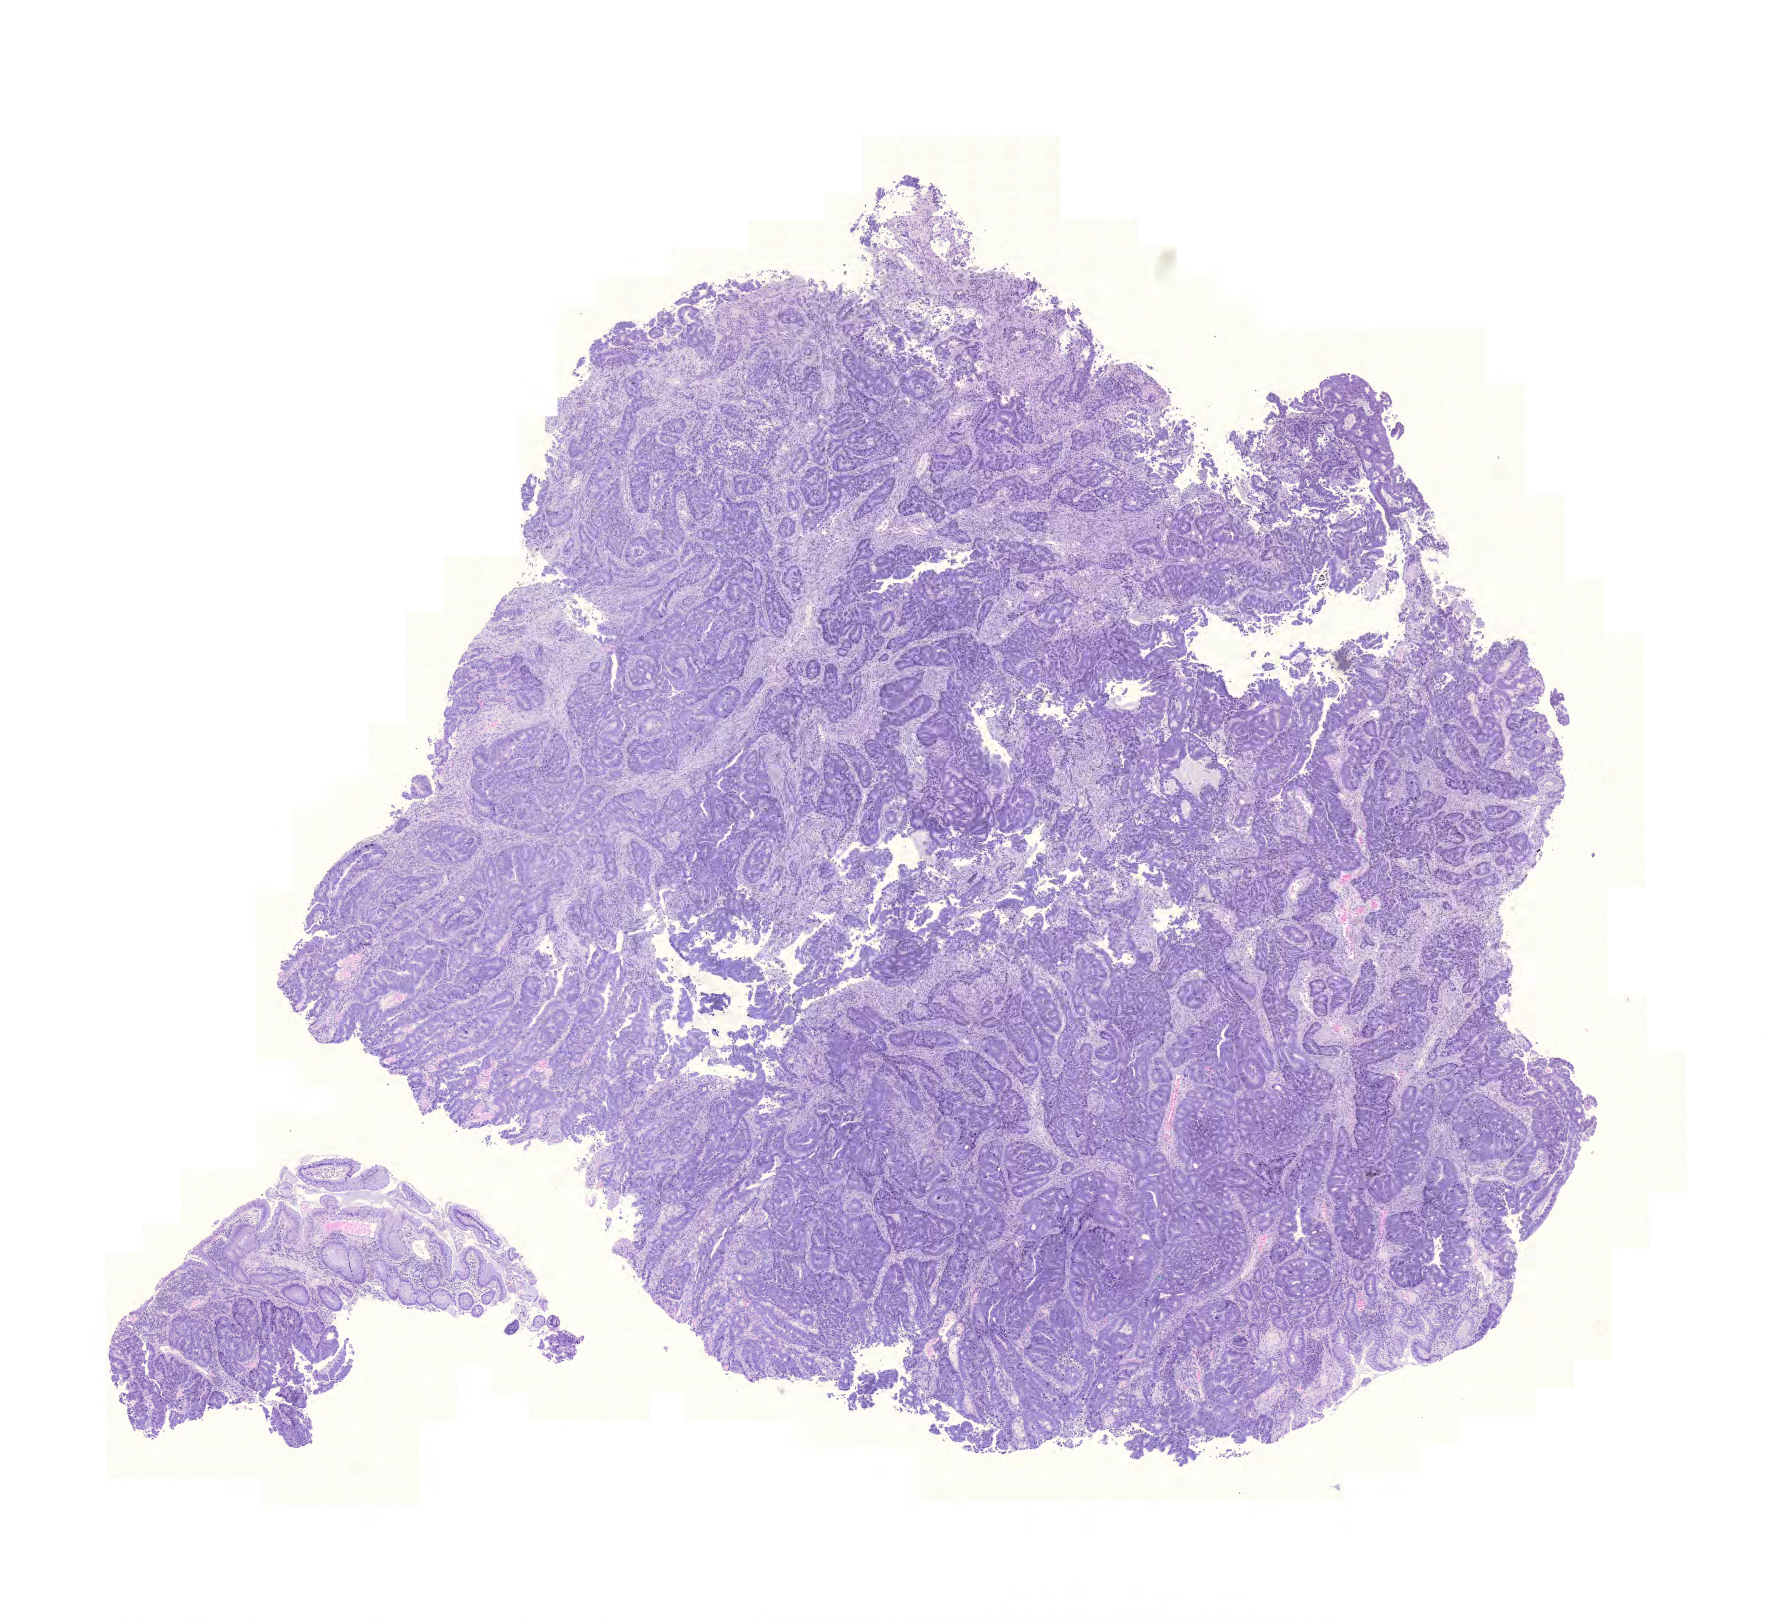
Whole-slide histology image, Hematoxylin and eosin (H&E) stained, whole scanned area (about 13.2 x 12.1 mm) shown as a low-resolution overview, FFPE section, sample: primary tumour, colon. Female patient; age at initial diagnosis 82 years.
Diagnosis: Adenocarcinoma, NOS (sigmoid colon).